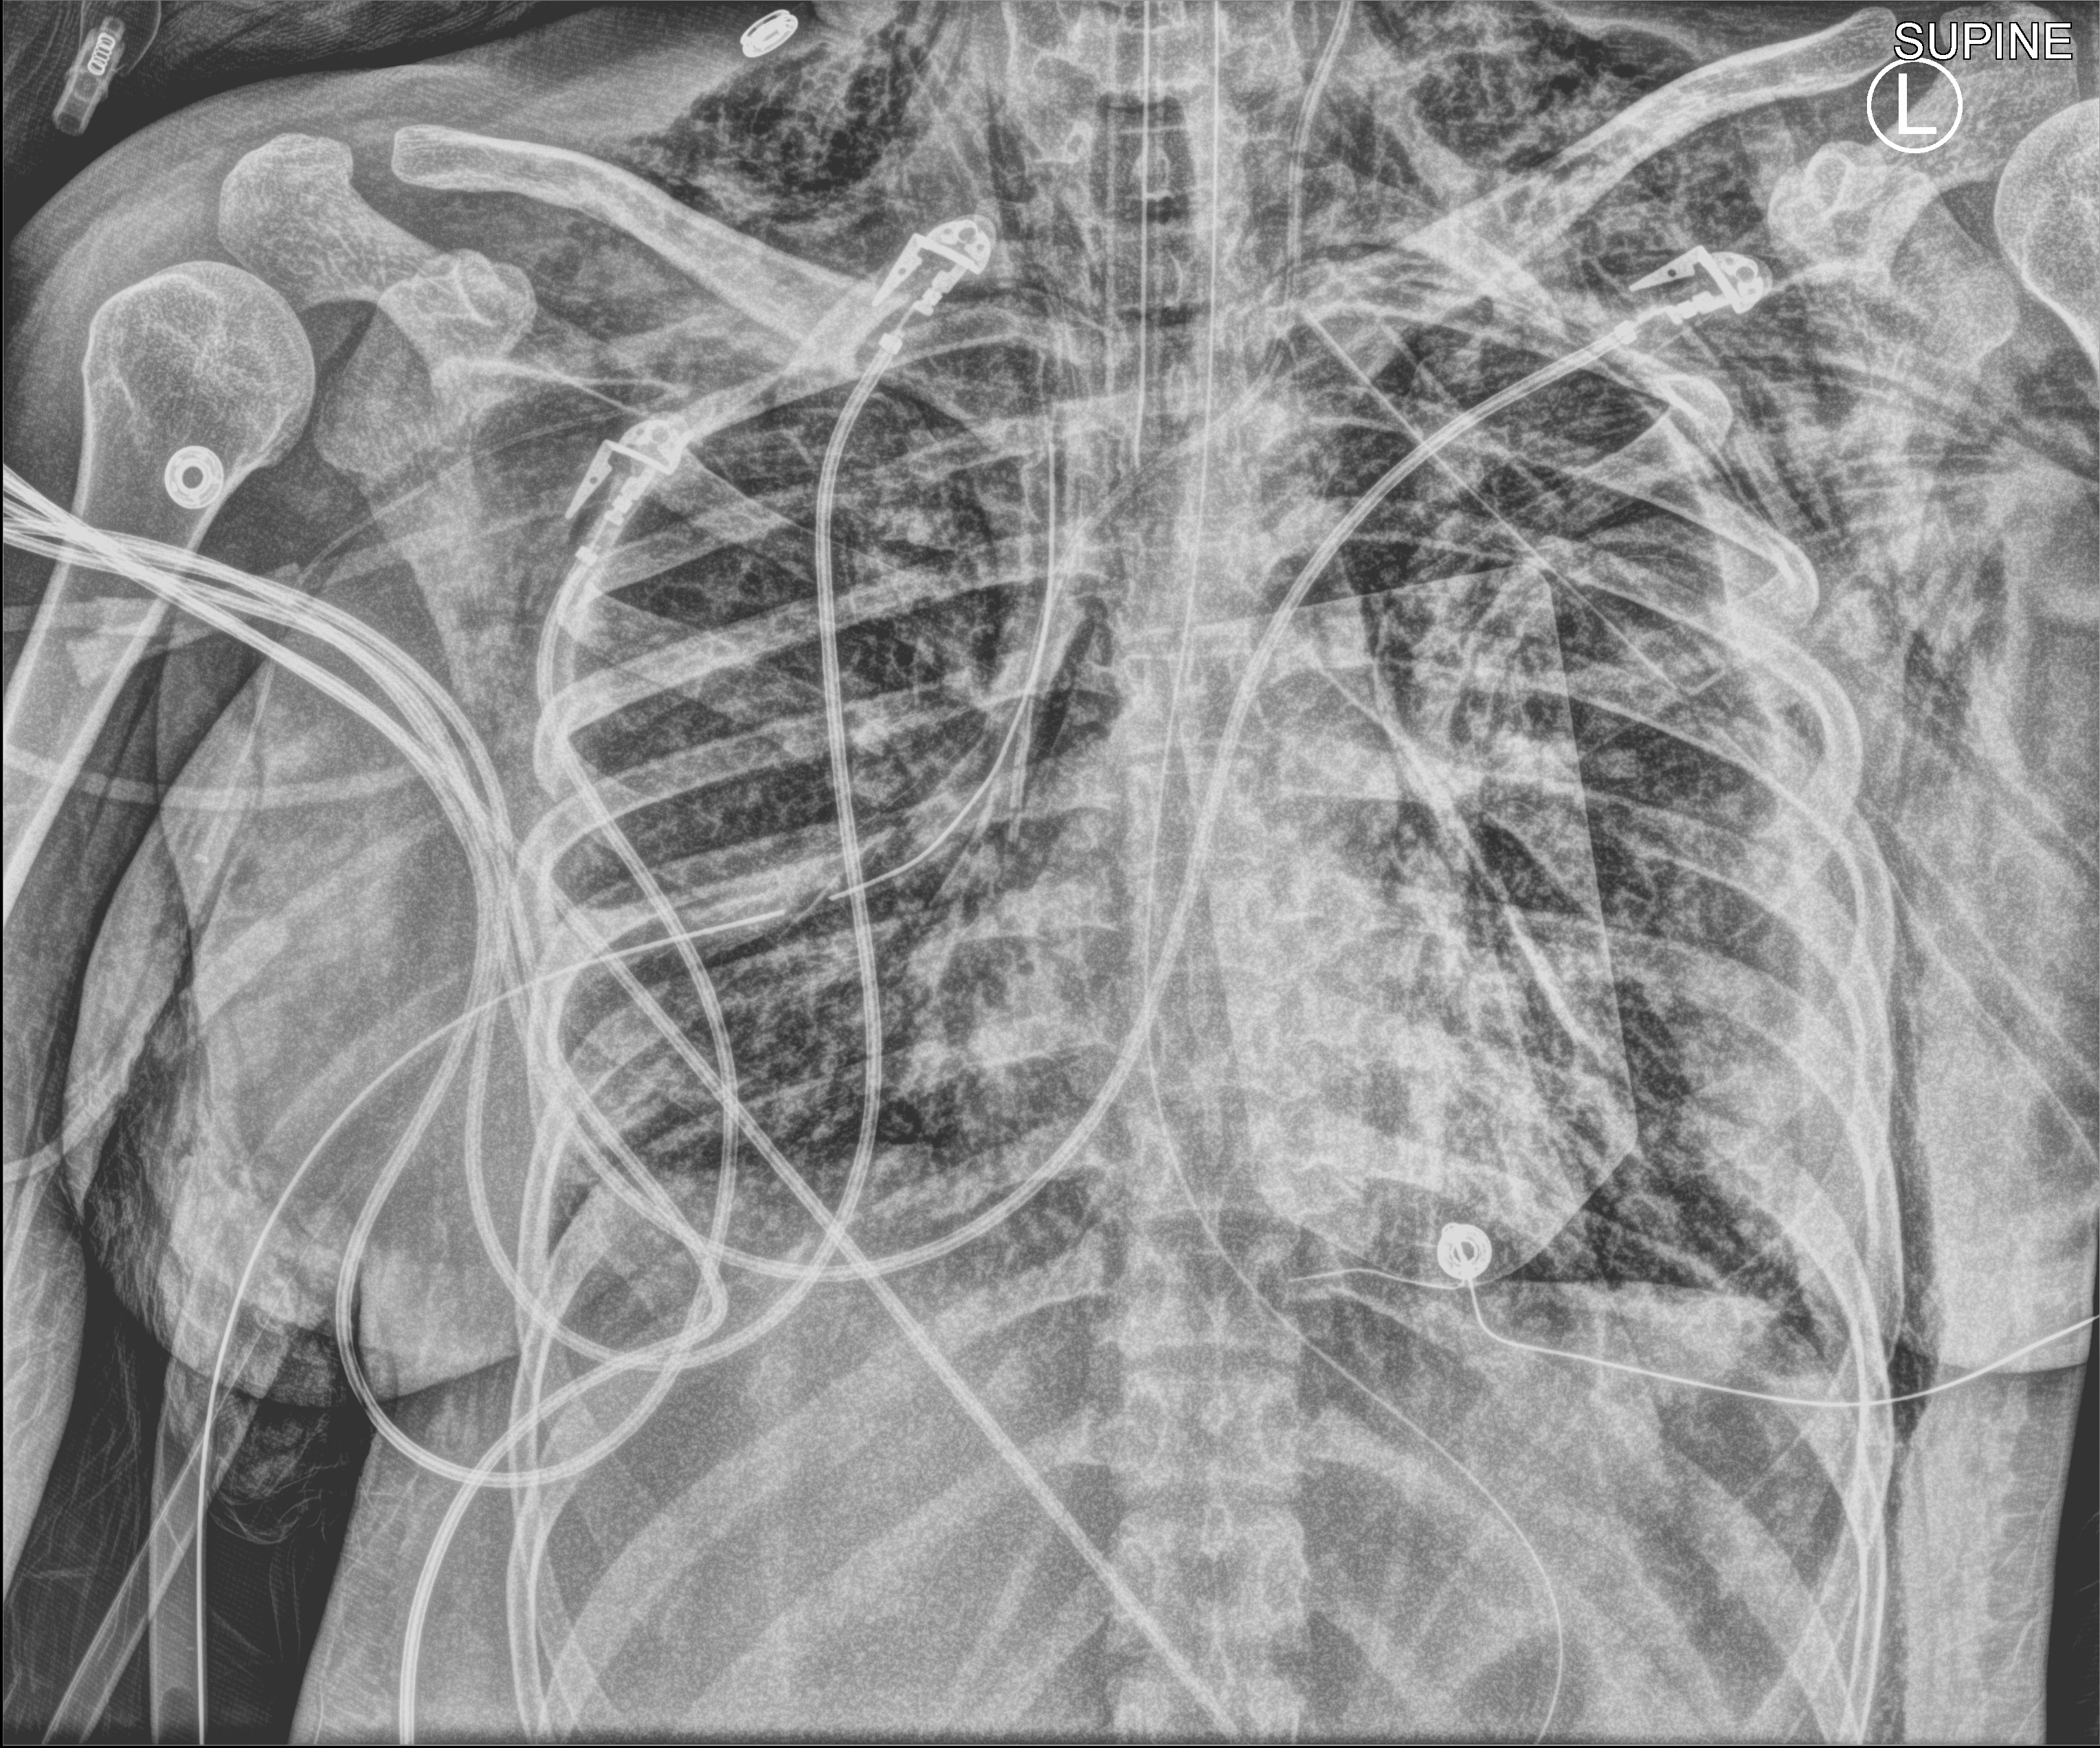
Chest X-ray (portable); anteroposterior (AP) projection. Adult patient hospitalised with COVID-19, age 18–59 years.
From the hospital-stay record, not from the radiograph (when in the stay this image was taken is not recorded):
- mechanically ventilated during this hospital stay: yes
- length of hospital stay: 30 days